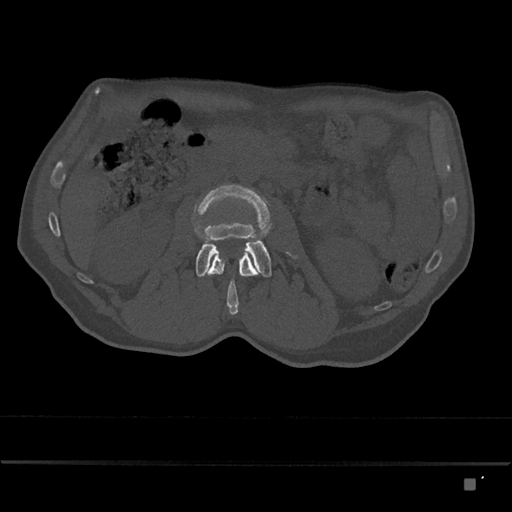
CT including the spine, one axial slice; slice 437 of 797 in the series (ordered by position); reconstruction kernel Br40s/3; 120 kVp; bone window (W 1800 / L 400 HU); 0.5 mm slice thickness; 512 × 512 image matrix, field of view 390 × 390 mm. Patient: male, 72 years. From the clinical record (not read from this slice): primary cancer: prostate.
Outlined on this slice (semi-automatic segmentation, software-assisted and operator-edited):
- L2 vertebra: bounding box [x1, y1, x2, y2] px = [204, 248, 258, 315]
- L3 vertebra: [194, 184, 297, 278]